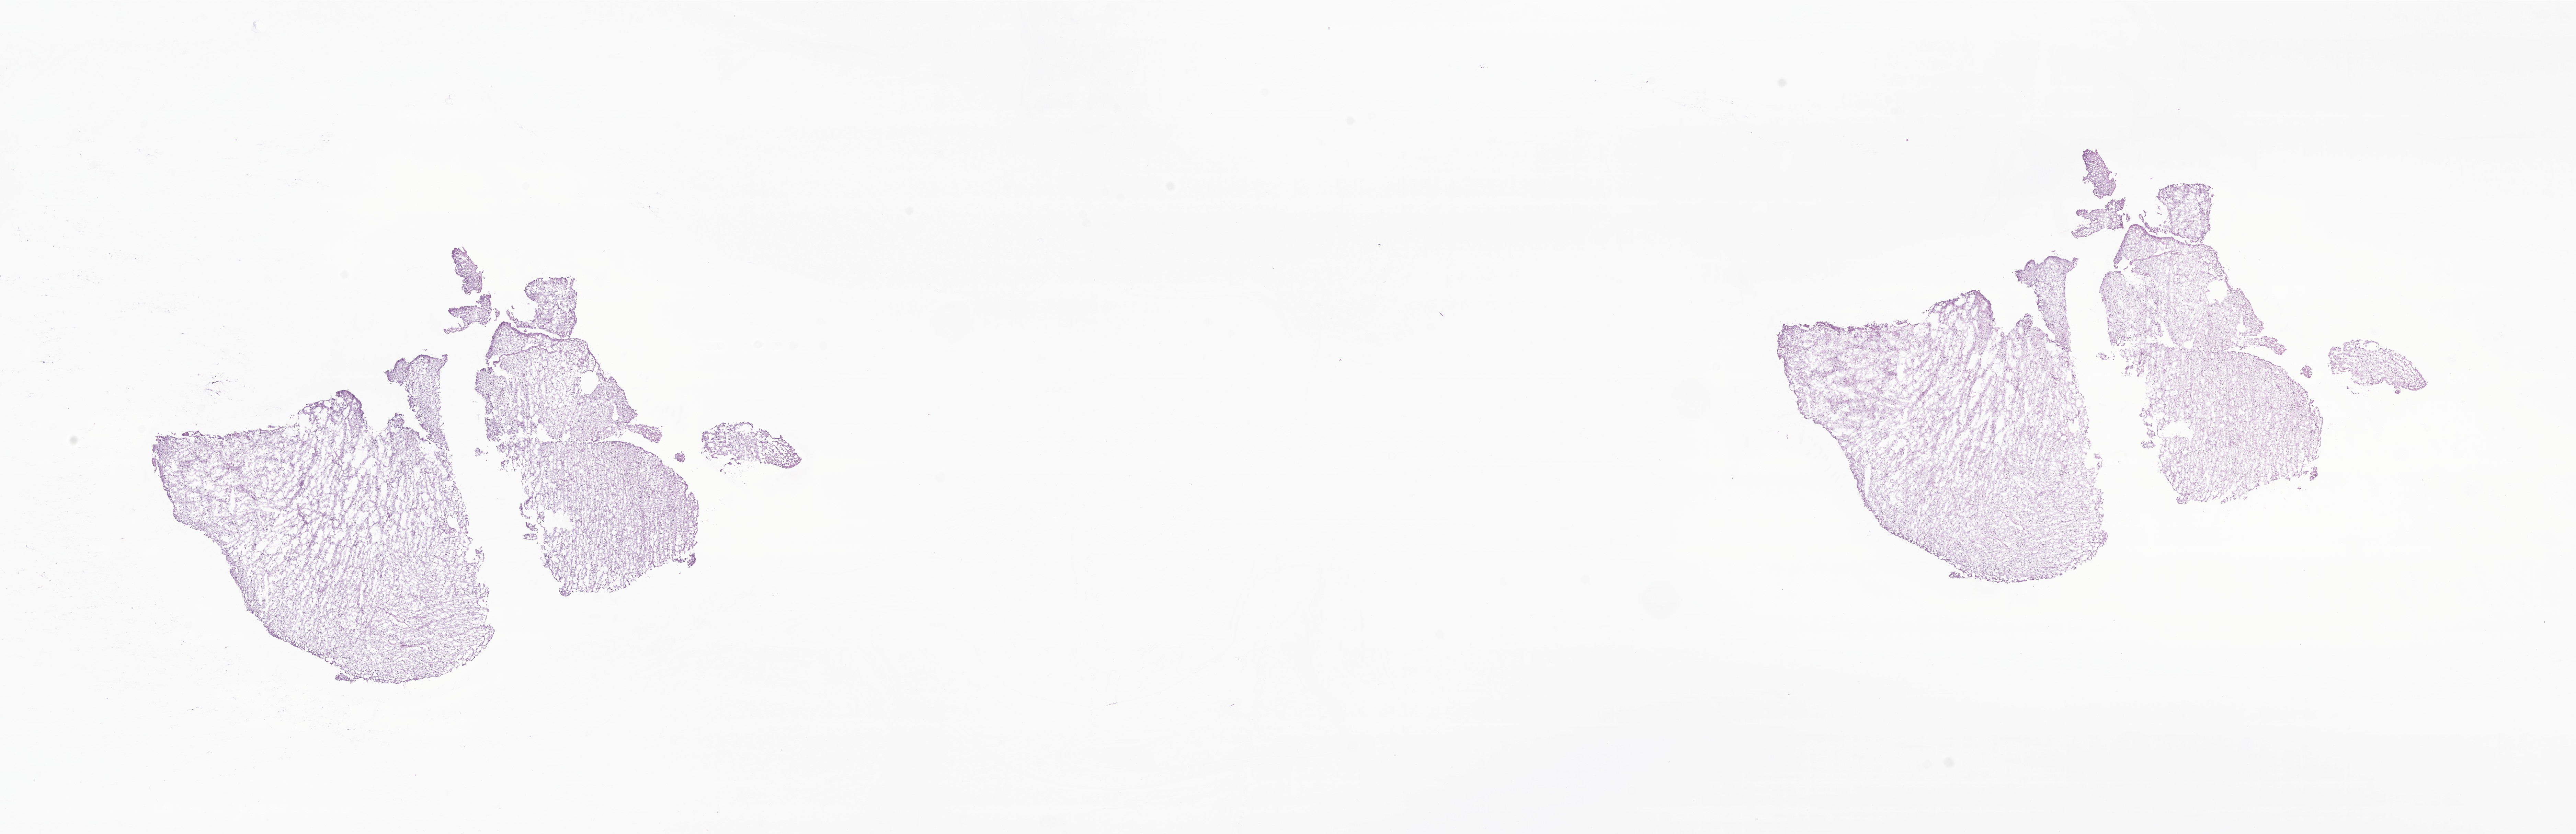
Whole-slide image, H&E stain of tumor tissue from the brain, shown as a low-resolution overview of the whole scanned area (about 31.6 x 10.2 mm), cryosection (OCT / tissue freezing medium). Male patient, age 79 months (6 years 7 months).
• recorded diagnosis: Pilocytic astrocytoma